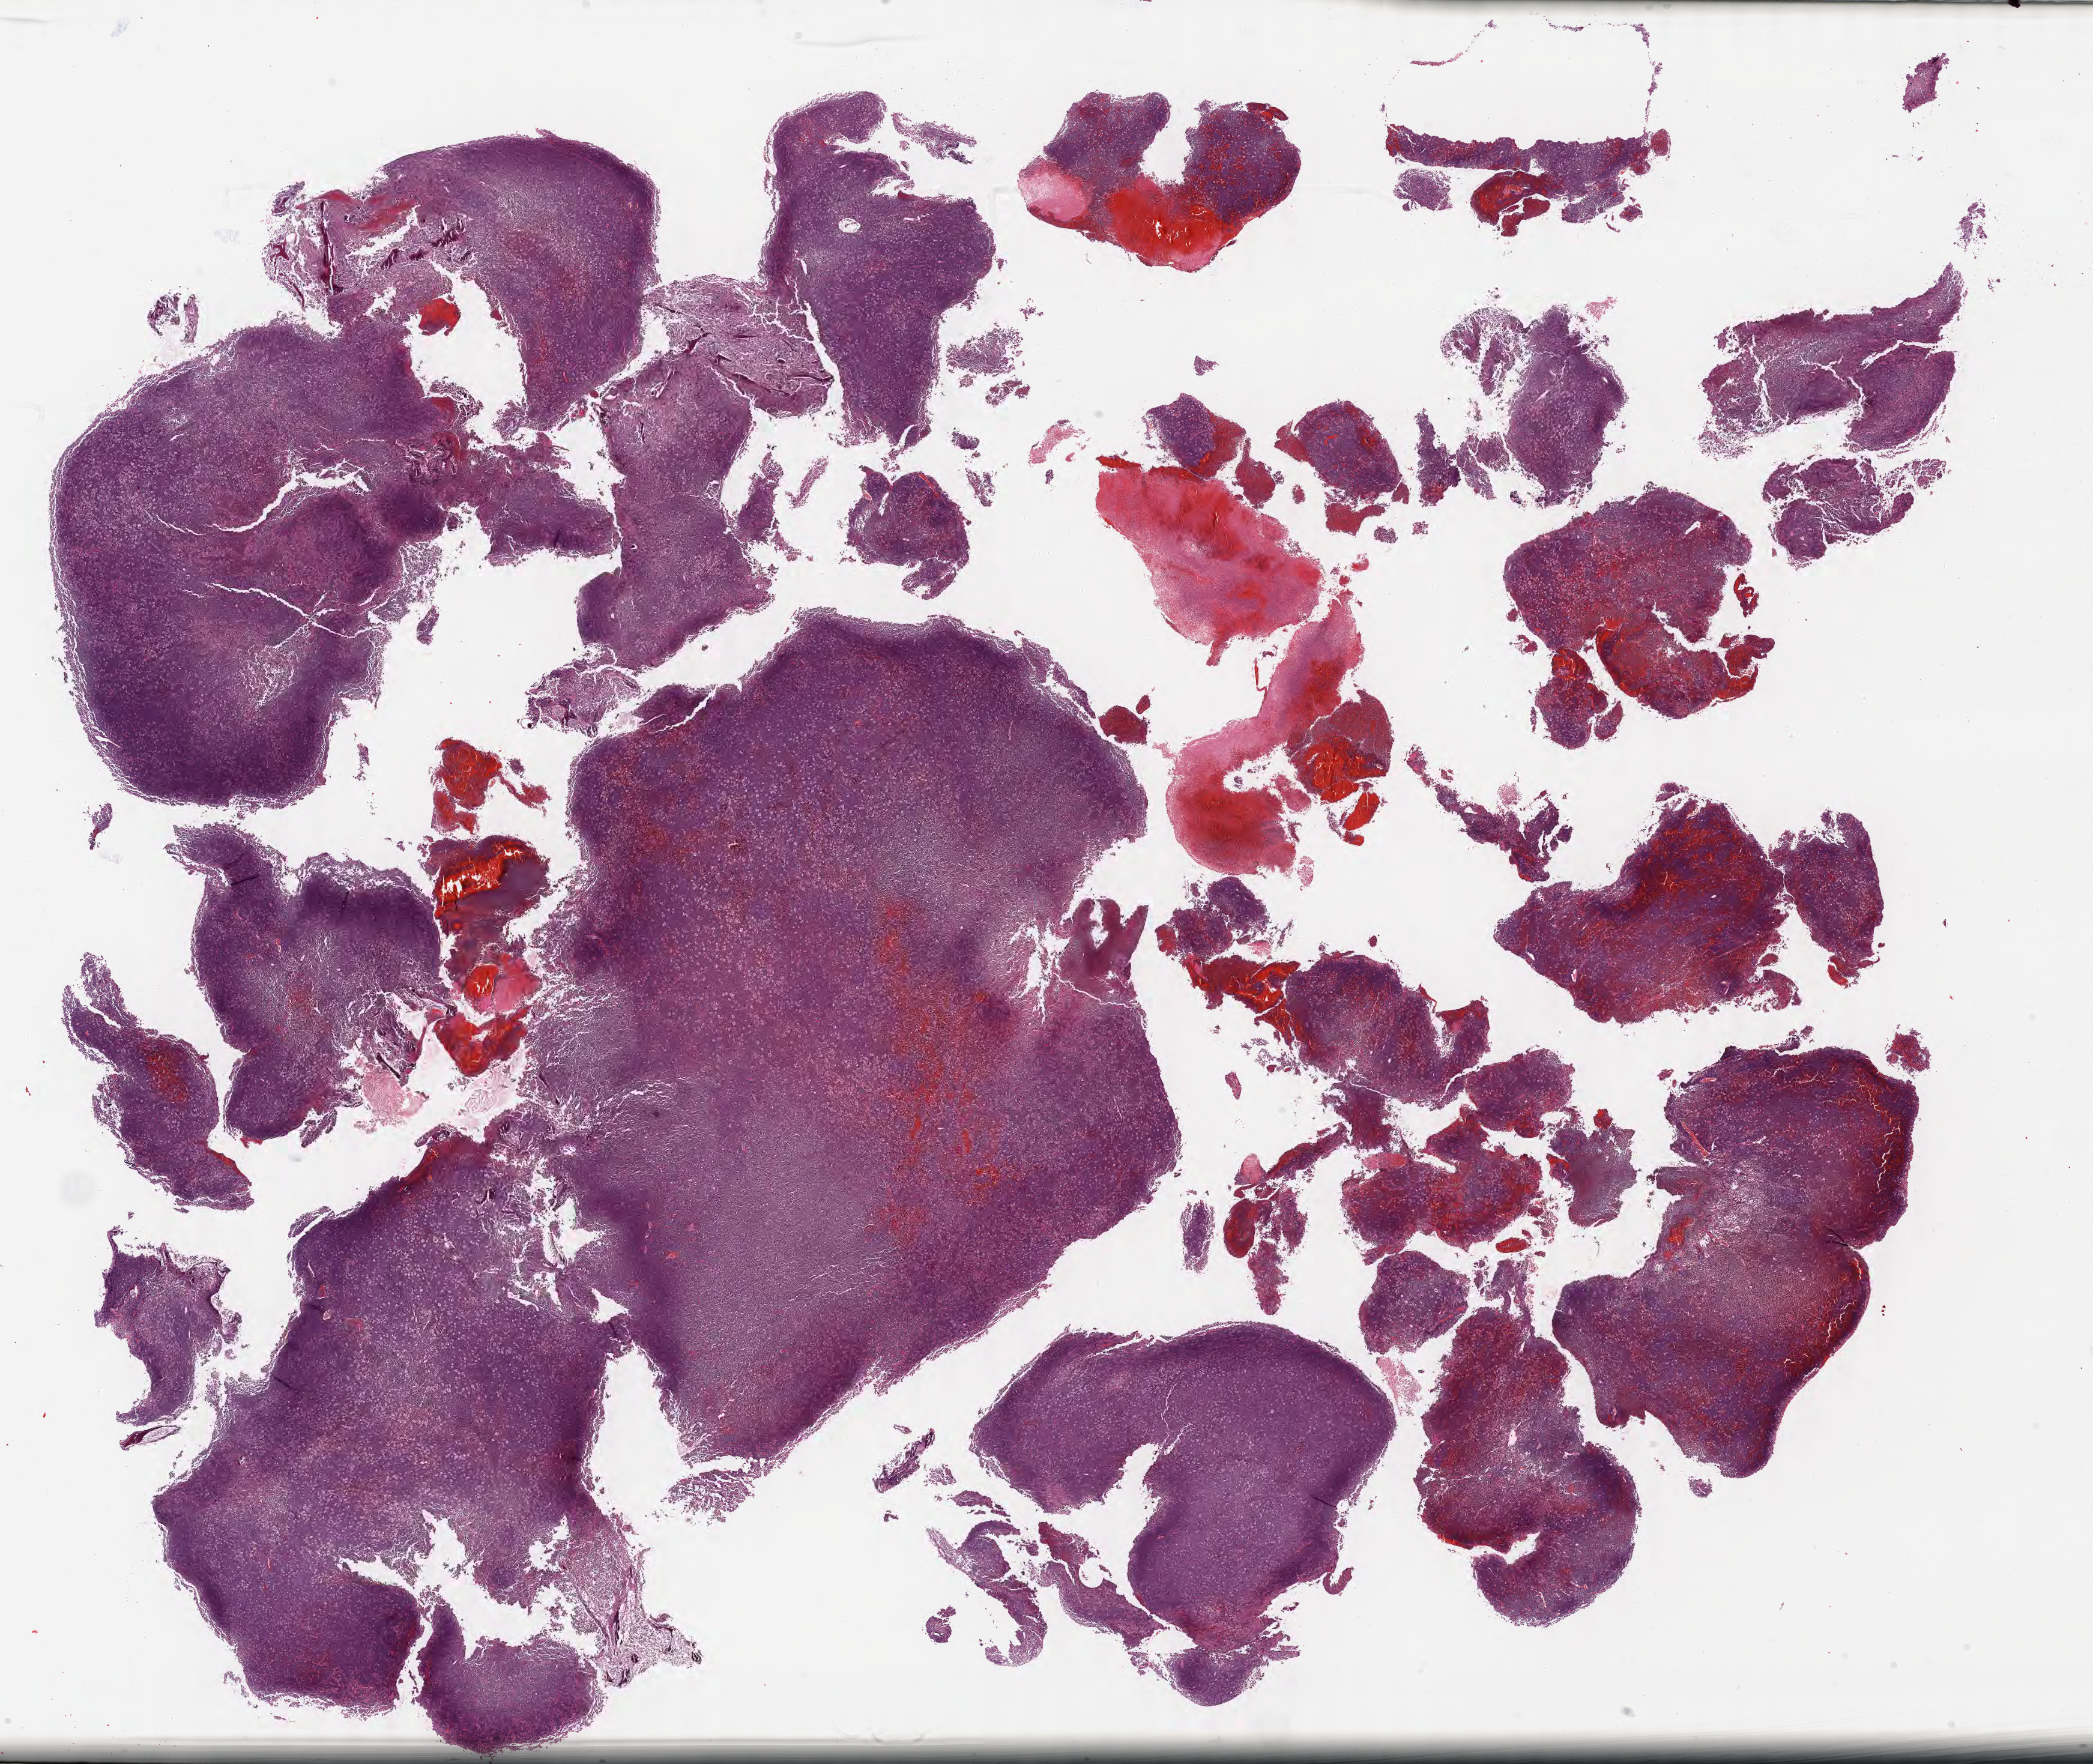
Digitized hematoxylin and eosin (H&E)-stained section, a low-resolution overview of the entire scanned area, about 28.2 x 23.7 mm, formalin-fixed paraffin-embedded section, specimen: primary tumor. Female, age 6 years at initial diagnosis. Pathologist review of this section (percent, as recorded): tumor cells 95%, tumor nuclei 95%, stromal cells 0%, necrosis 5%, normal cells 0%. Infiltration values recorded for this section: lymphocyte infiltration 20%, monocyte infiltration 50%, neutrophil infiltration 10%.
• Ann Arbor stage (patient): Stage IV
• diagnosis: Burkitt lymphoma, NOS